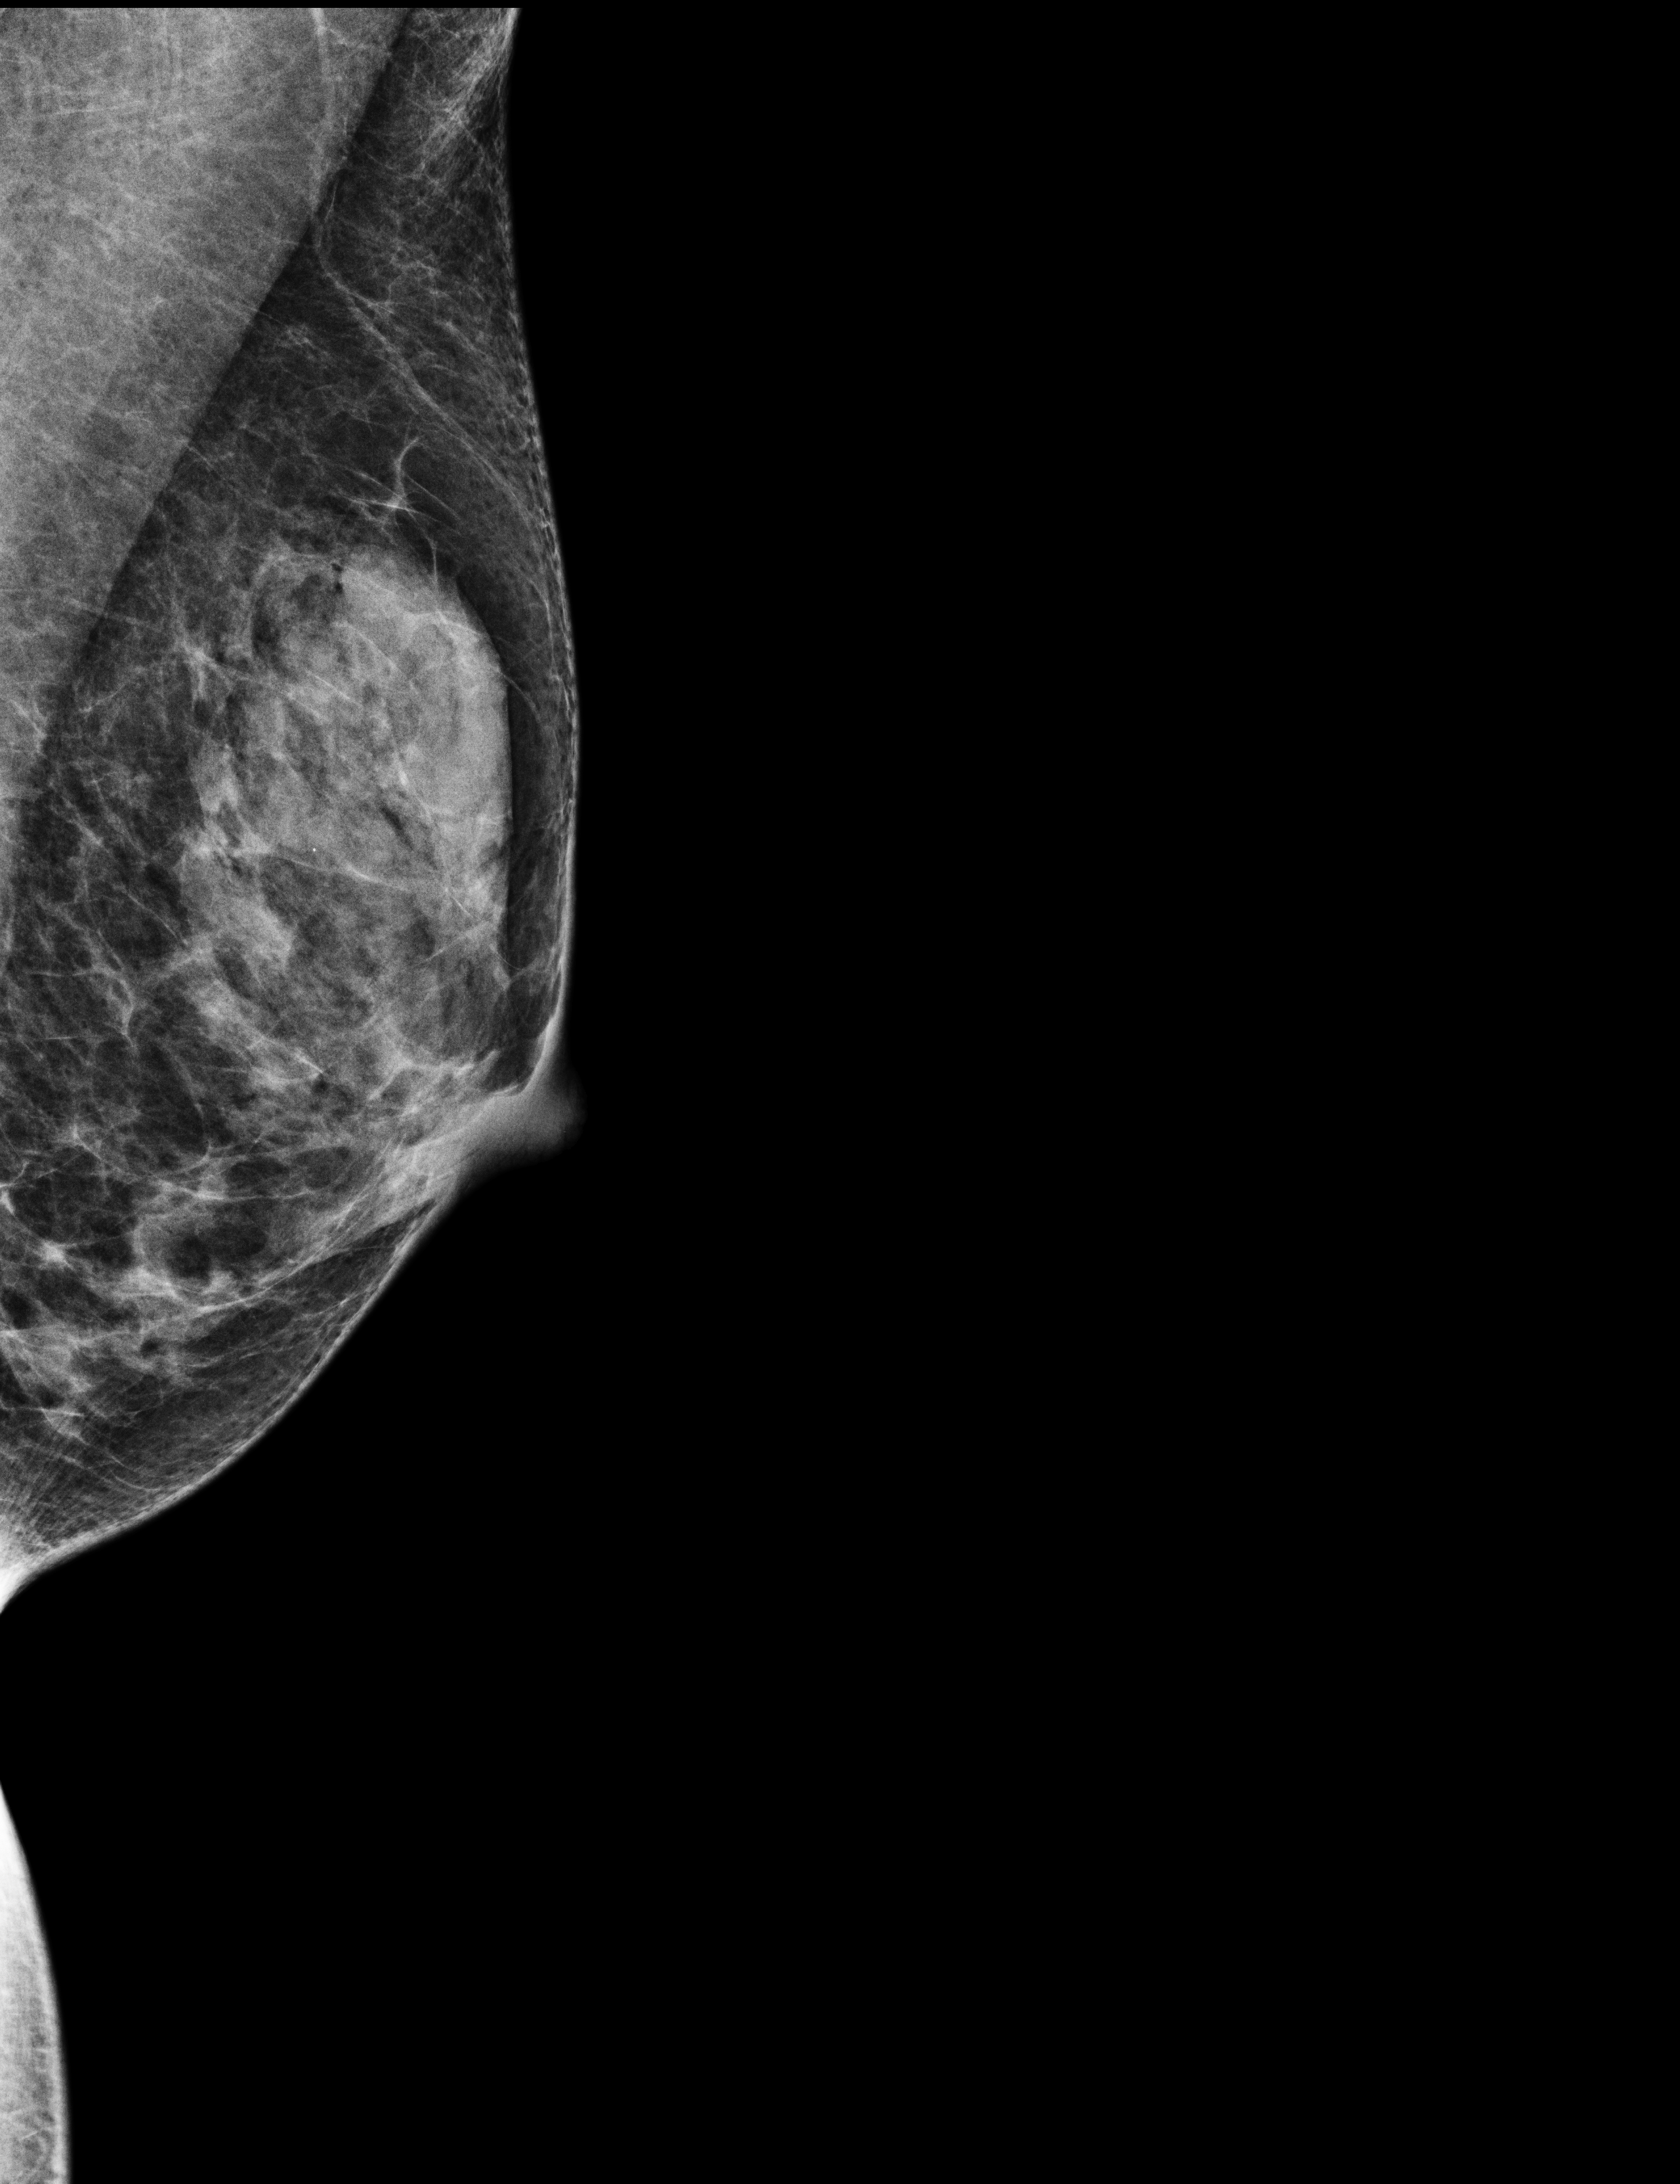
Screening examination. Female patient, age 61 years.
Image type: full-field digital mammogram. Breast: left. Projection: mediolateral oblique (MLO) view.